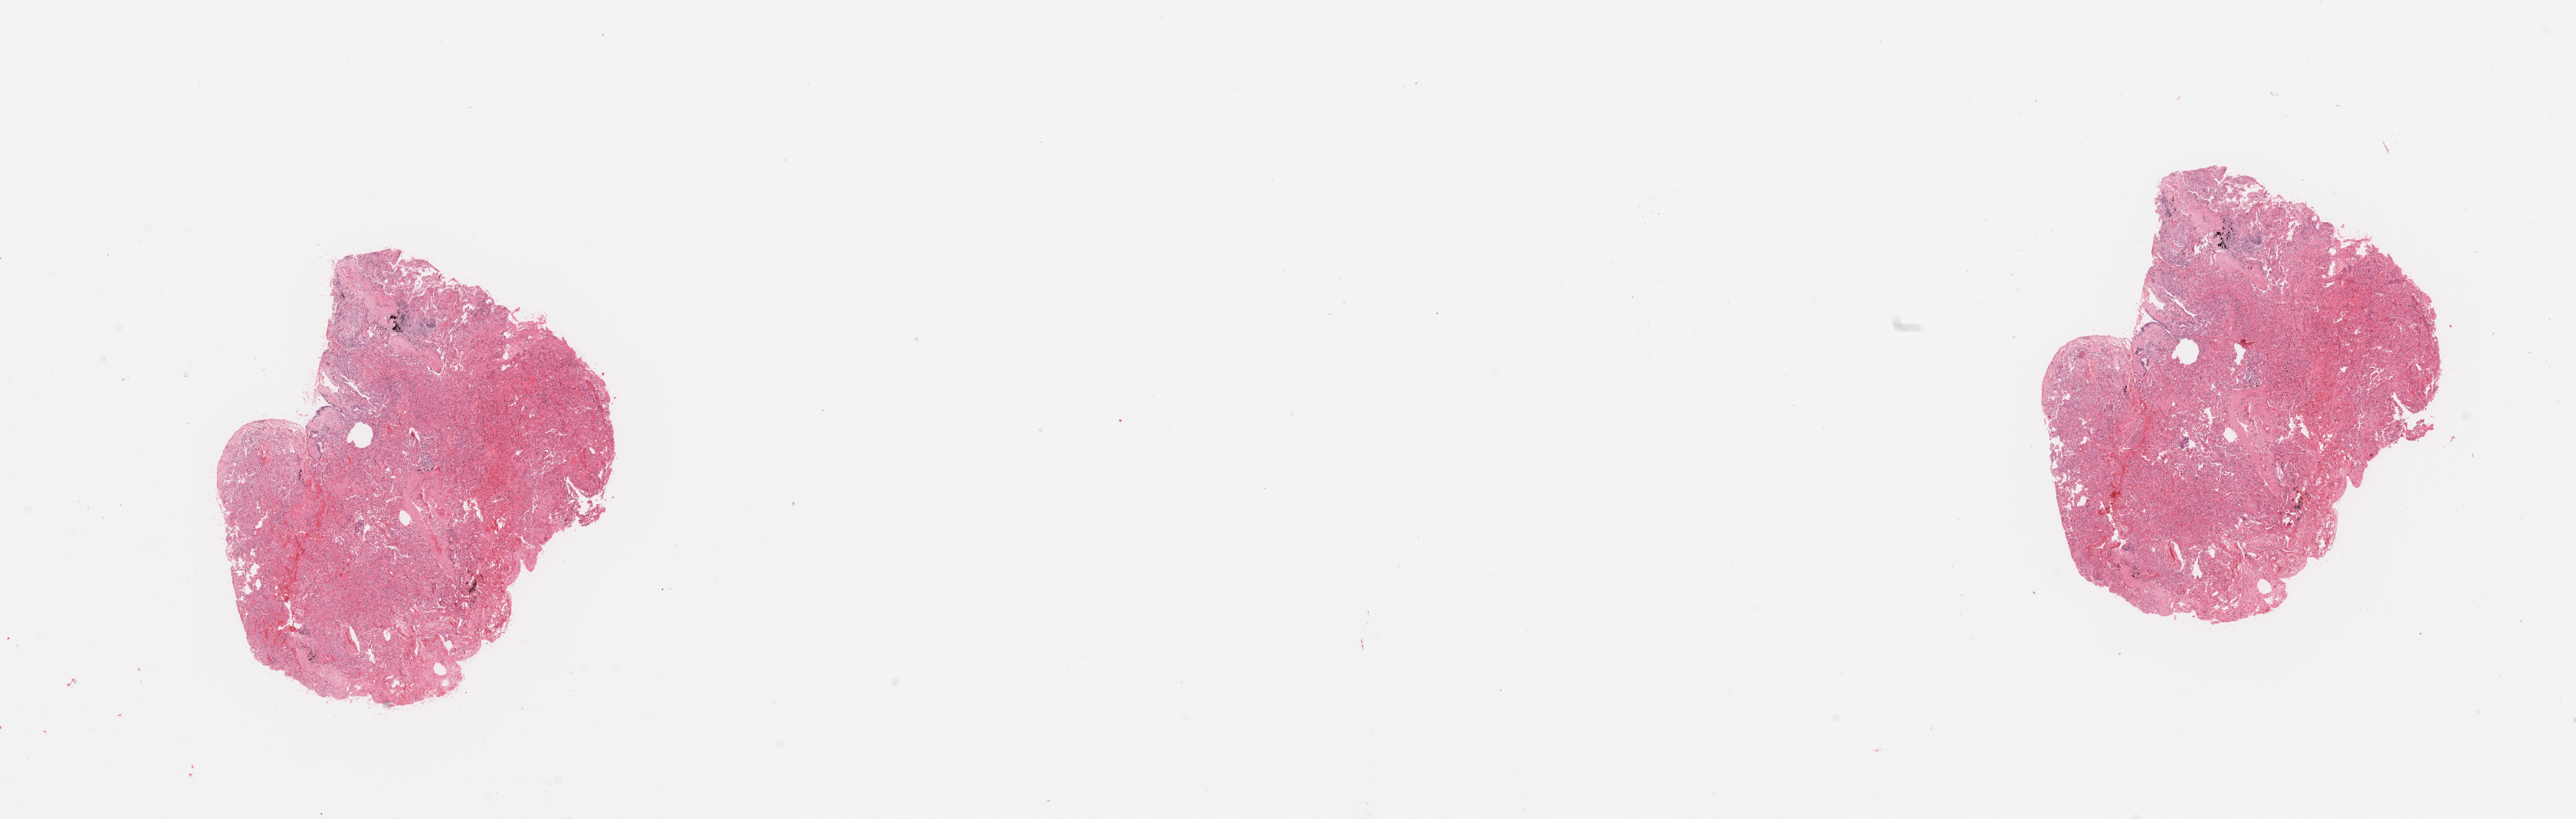
Digitized H&E tissue section (whole slide) — shown as a low-resolution overview of the whole scanned area (about 26.6 x 8.5 mm, slide scanned at 20x). Normal (non-tumour) tissue sample, sampled site: lung. Female, 78 y/o.
* this section: normal (non-tumour) tissue from the same patient
* patient diagnosis: Adenocarcinoma, NOS